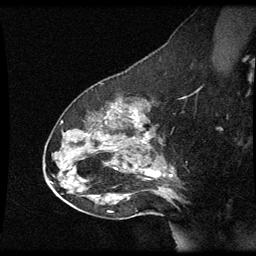
Breast MRI (dynamic contrast-enhanced), one sagittal slice. Slice 38 of 60 in the series (ordered by position). Dynamic contrast-enhanced series, image 2 of 3 at this slice position (ordered by acquisition). 1.5 T. TE 4.2 ms, TR 8.9 ms. 2 mm slice thickness. 256 × 256 image matrix, field of view 200 × 200 mm. Female patient, age 49 years. Case-level facts recorded for this patient, not image findings: setting: breast cancer imaged before/during neoadjuvant chemotherapy; receptor status: HR-positive, HER2-negative.
Structures marked on this image (semi-automatically segmented with operator editing):
- analysis volume of interest (the breast-tissue region the enhancement analysis was run in; not a lesion): bounding box <46,92,177,205> (left, top, right, bottom; pixels)
- tumour enhancement mask (voxels above the 70 % enhancement threshold inside the analysis volume of interest): <133,110,172,177>